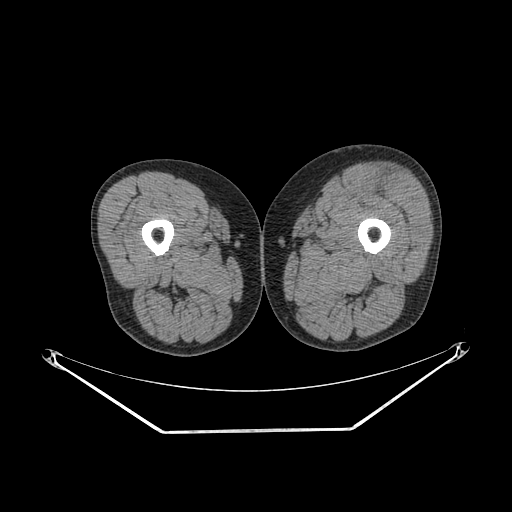
CT of an extremity soft-tissue mass (from a PET/CT study), one axial slice; position 219 of 267 along the scan axis; reconstruction kernel SOFT; 140 kVp; soft-tissue window (W 400 / L 40 HU); 3.75 mm slice thickness; 512 × 512 image matrix. Male patient. From the clinical record (not read from this slice): histological type: extraskeletal osteosarcoma; grade: high; site of the primary tumour: thigh.
Annotated regions visible in this slice (expert contour drawn on MRI and transferred to this co-registered scan by the dataset authors):
- gross tumour volume (mass): bounding box [x1, y1, x2, y2] px = [379, 176, 400, 202]